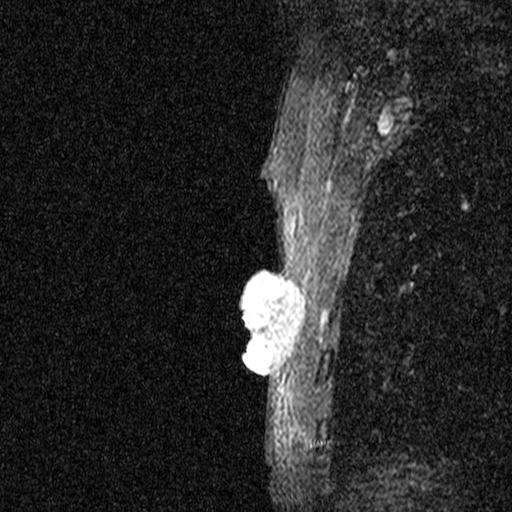
Breast MRI (dynamic contrast-enhanced), one sagittal slice; position 39 of 44 along the scan axis; dynamic contrast-enhanced study with each time point stored as its own series, time point 2 of 3 at this slice position (early post-contrast, ordered by acquisition time); 1.5 T; TE 4.5 ms, TR 11 ms; 2.05 mm slice thickness; 512 × 512 image matrix. Female patient, age 44 years. Case-level facts recorded for this patient, not image findings: setting: breast cancer imaged before/during neoadjuvant chemotherapy; receptor status: HR-positive, HER2-negative.
Structures marked on this image (semi-automatically segmented with operator editing):
- analysis volume of interest (the breast-tissue region the enhancement analysis was run in; not a lesion): box from (x=204, y=254) to (x=316, y=401) px
- tumour enhancement mask (voxels above the 90 % enhancement threshold inside the analysis volume of interest): (x=240, y=259)–(x=300, y=397)